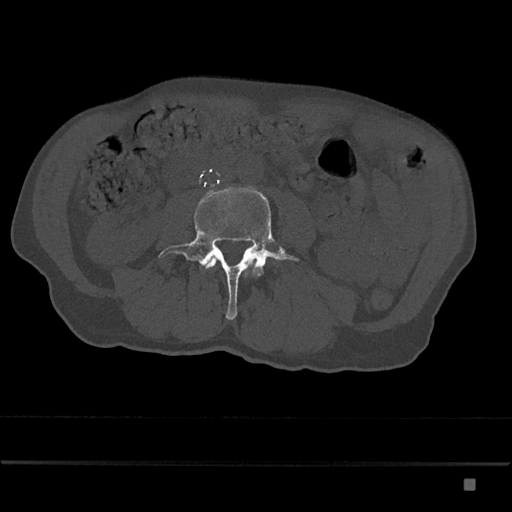
CT including the spine, one axial slice; position 349 of 797 along the scan axis; bone window (W 1800 / L 400 HU); 512 × 512 image matrix, field of view 390 × 390 mm. Patient: male, 72 years. Case-level facts recorded for this patient, not image findings: primary cancer: prostate.
Structures marked on this image (semi-automatic segmentation, software-assisted and operator-edited):
- L3 vertebra: bounding box [x1, y1, x2, y2] px = [206, 257, 255, 269]
- L4 vertebra: [159, 187, 299, 320]